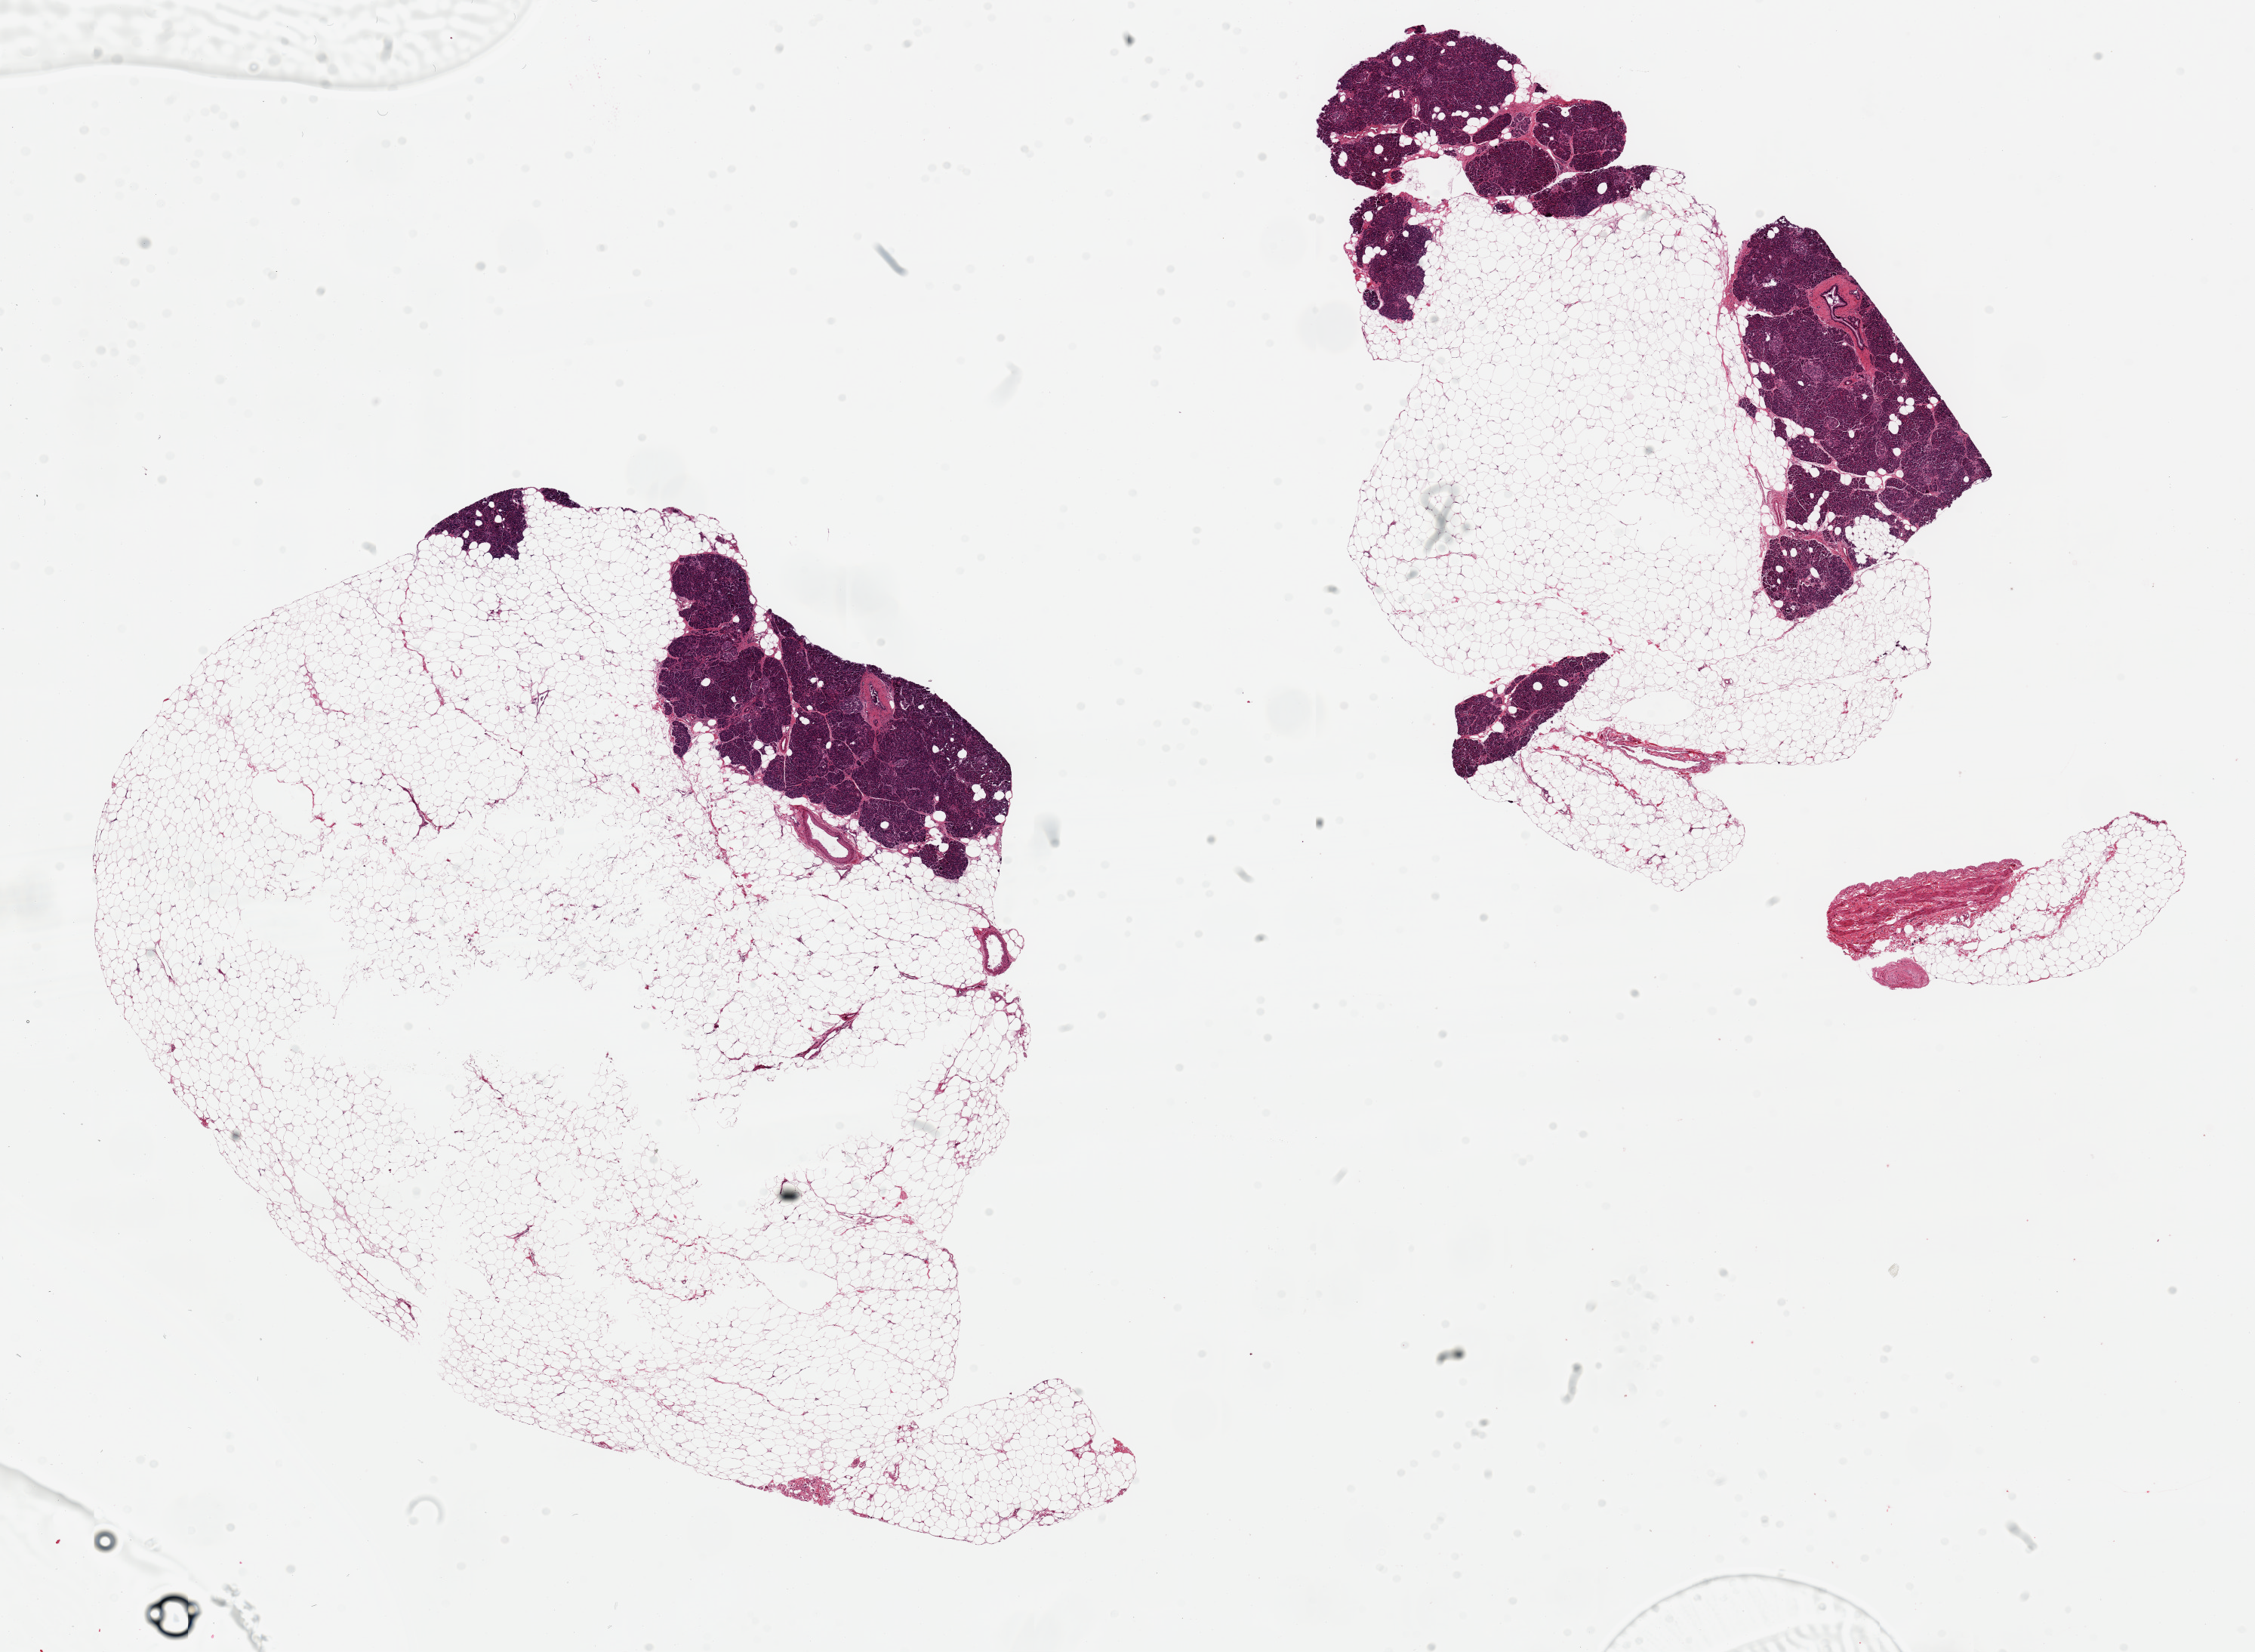
Whole-slide image, haematoxylin and eosin stain, shown as a low-resolution overview of the whole scanned area (about 23.6 x 17.3 mm, from a 20x scan). PAXgene-fixed paraffin-embedded (PFPE) section. Sampled site (target tissue): pancreas. Donor tissue sample. Male donor.
* pathologist's review note for this sample: 2 ~ 8x8mm pieces; only ~10% on one edge is pancreas, well-preserved. Rest is adipose tissue